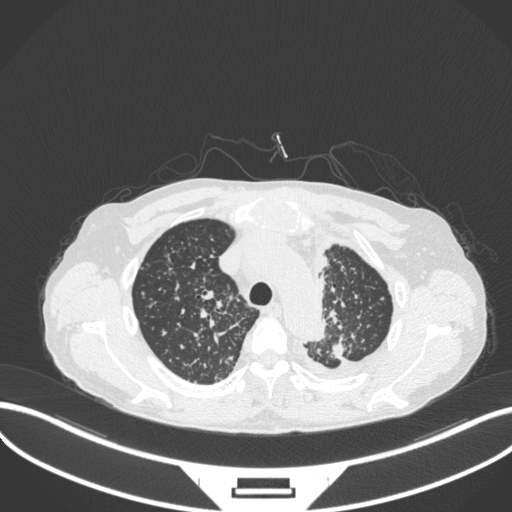
Chest CT, one axial slice; reconstruction kernel B31f; 120 kVp; lung window (W 1500 / L -600 HU); 1 mm slice thickness; 512 × 512 image matrix, field of view 400 × 400 mm. Male patient, age 58 years. From the clinical record (not read from this slice): clinical TNM (as recorded): T1c N3 M1.
Structures marked on this image (rectangle marked by the reading radiologist):
- lung tumour (recorded histology: adenocarcinoma): box from (x=326, y=337) to (x=351, y=363) px